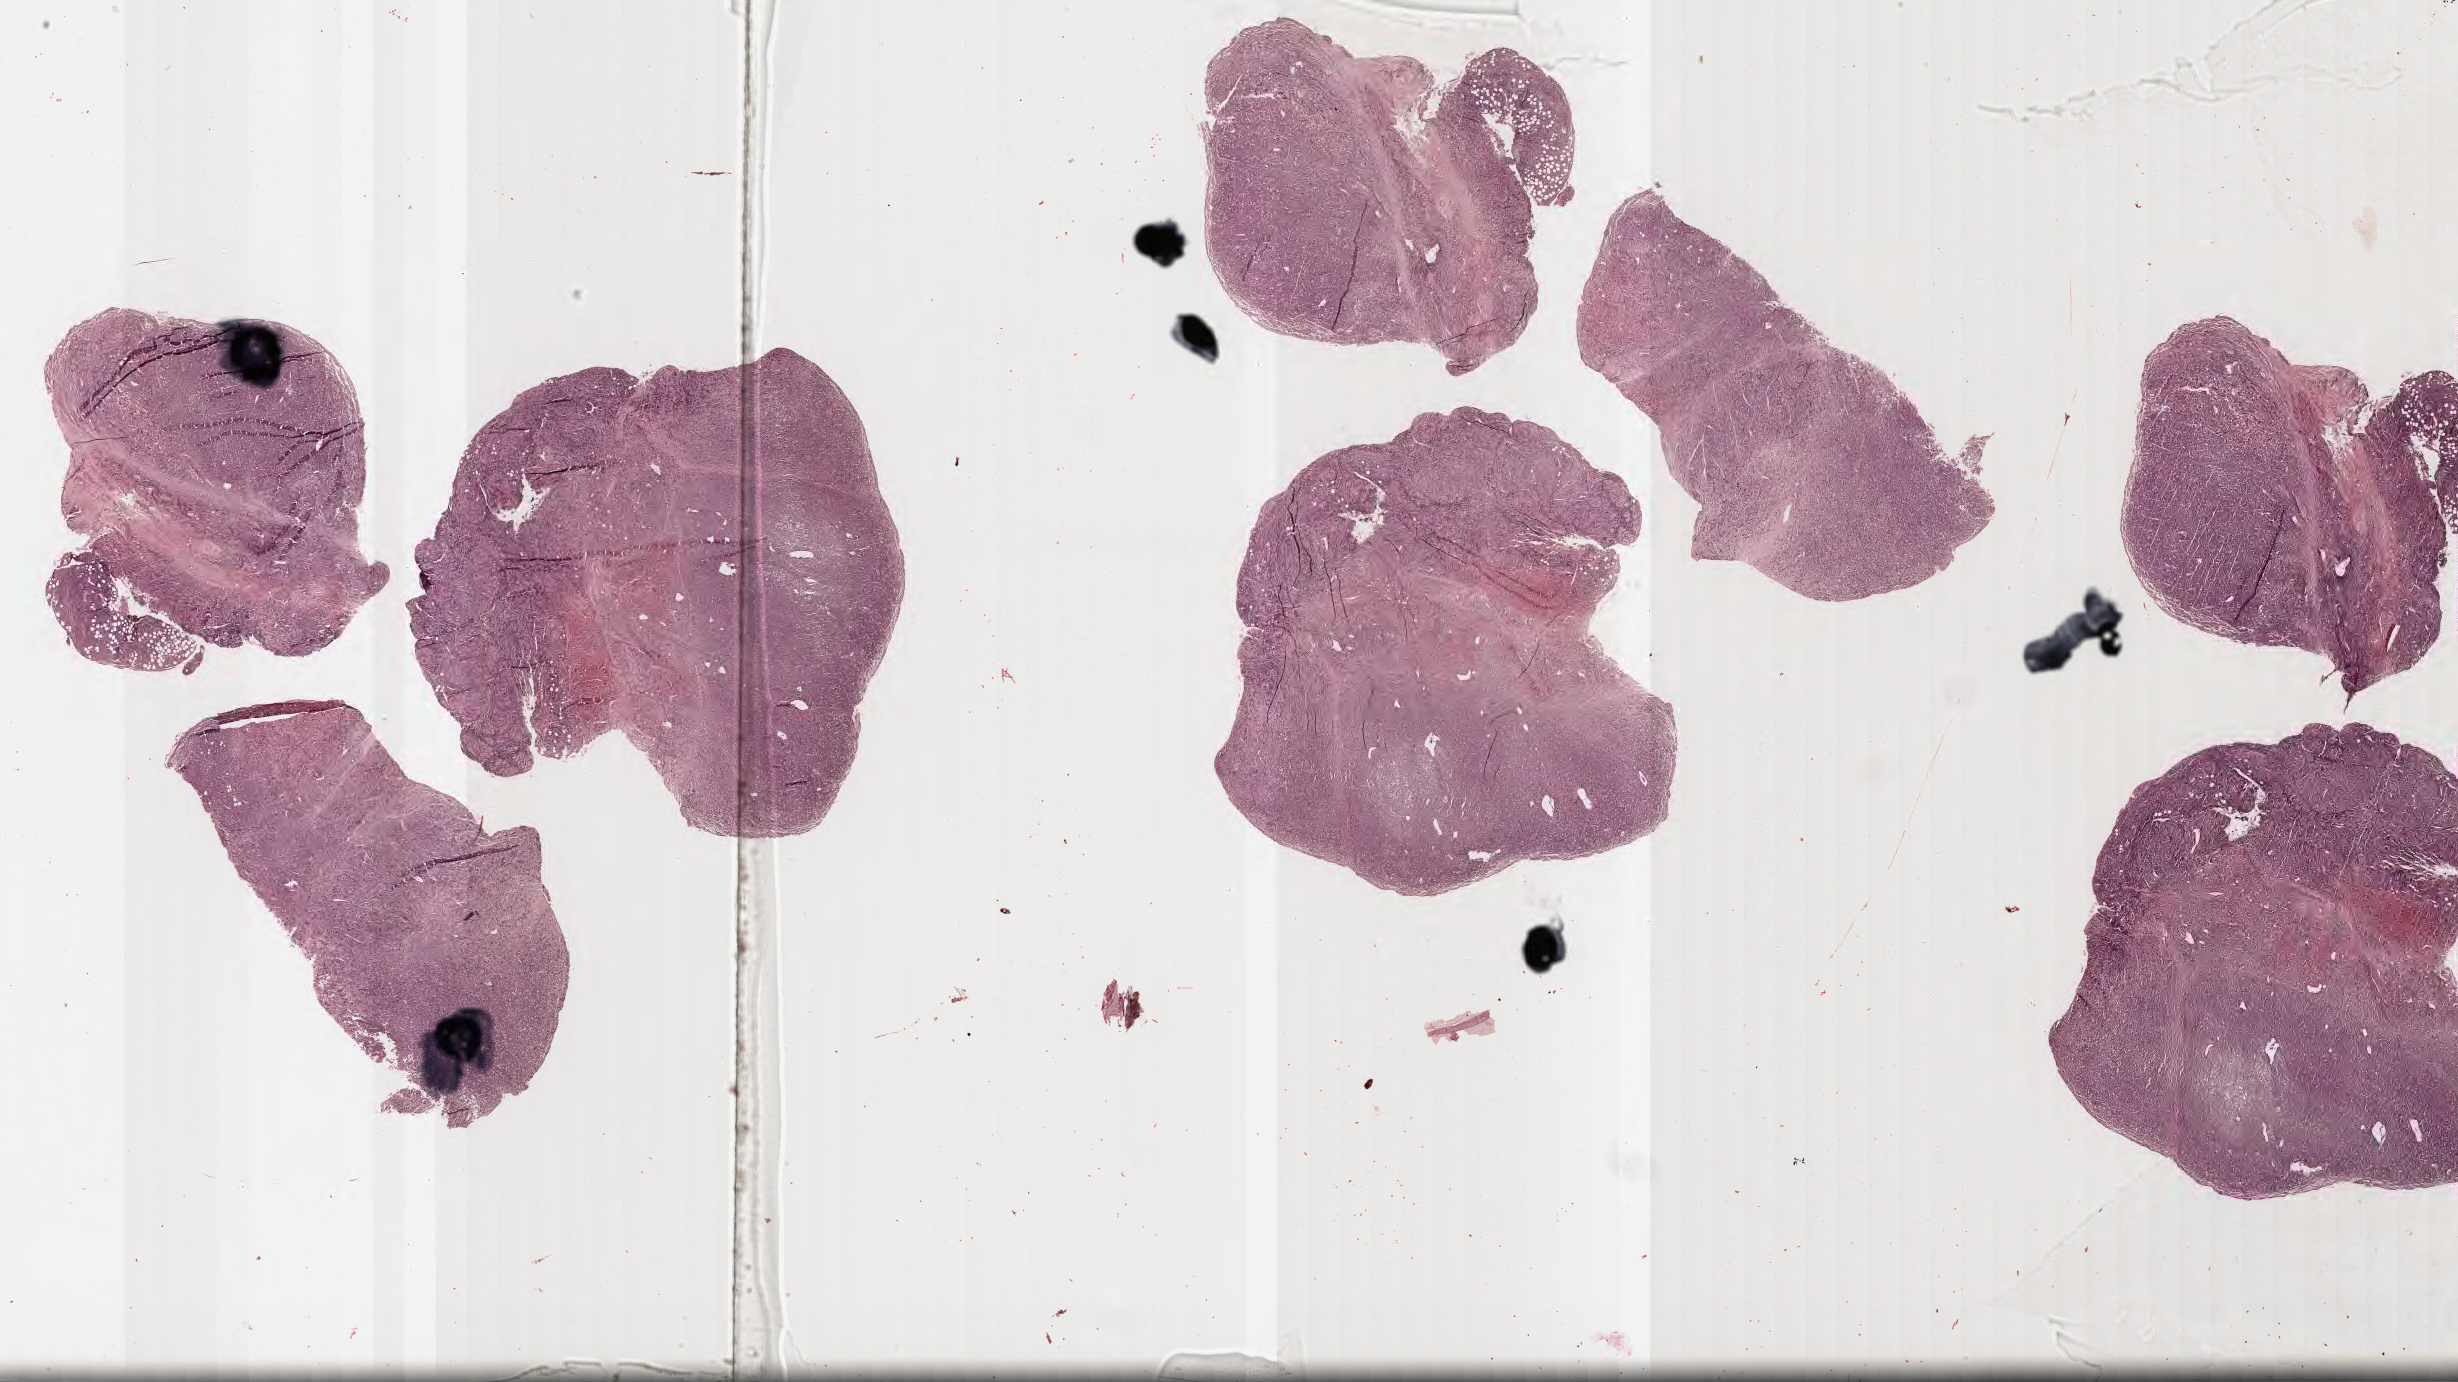
Digitized hematoxylin and eosin (H&E)-stained section, a low-resolution overview of the entire scanned area, about 39.8 x 22.4 mm. Specimen: tumor tissue. Patient male; aged 15.
Diagnosis: Burkitt lymphoma, NOS.